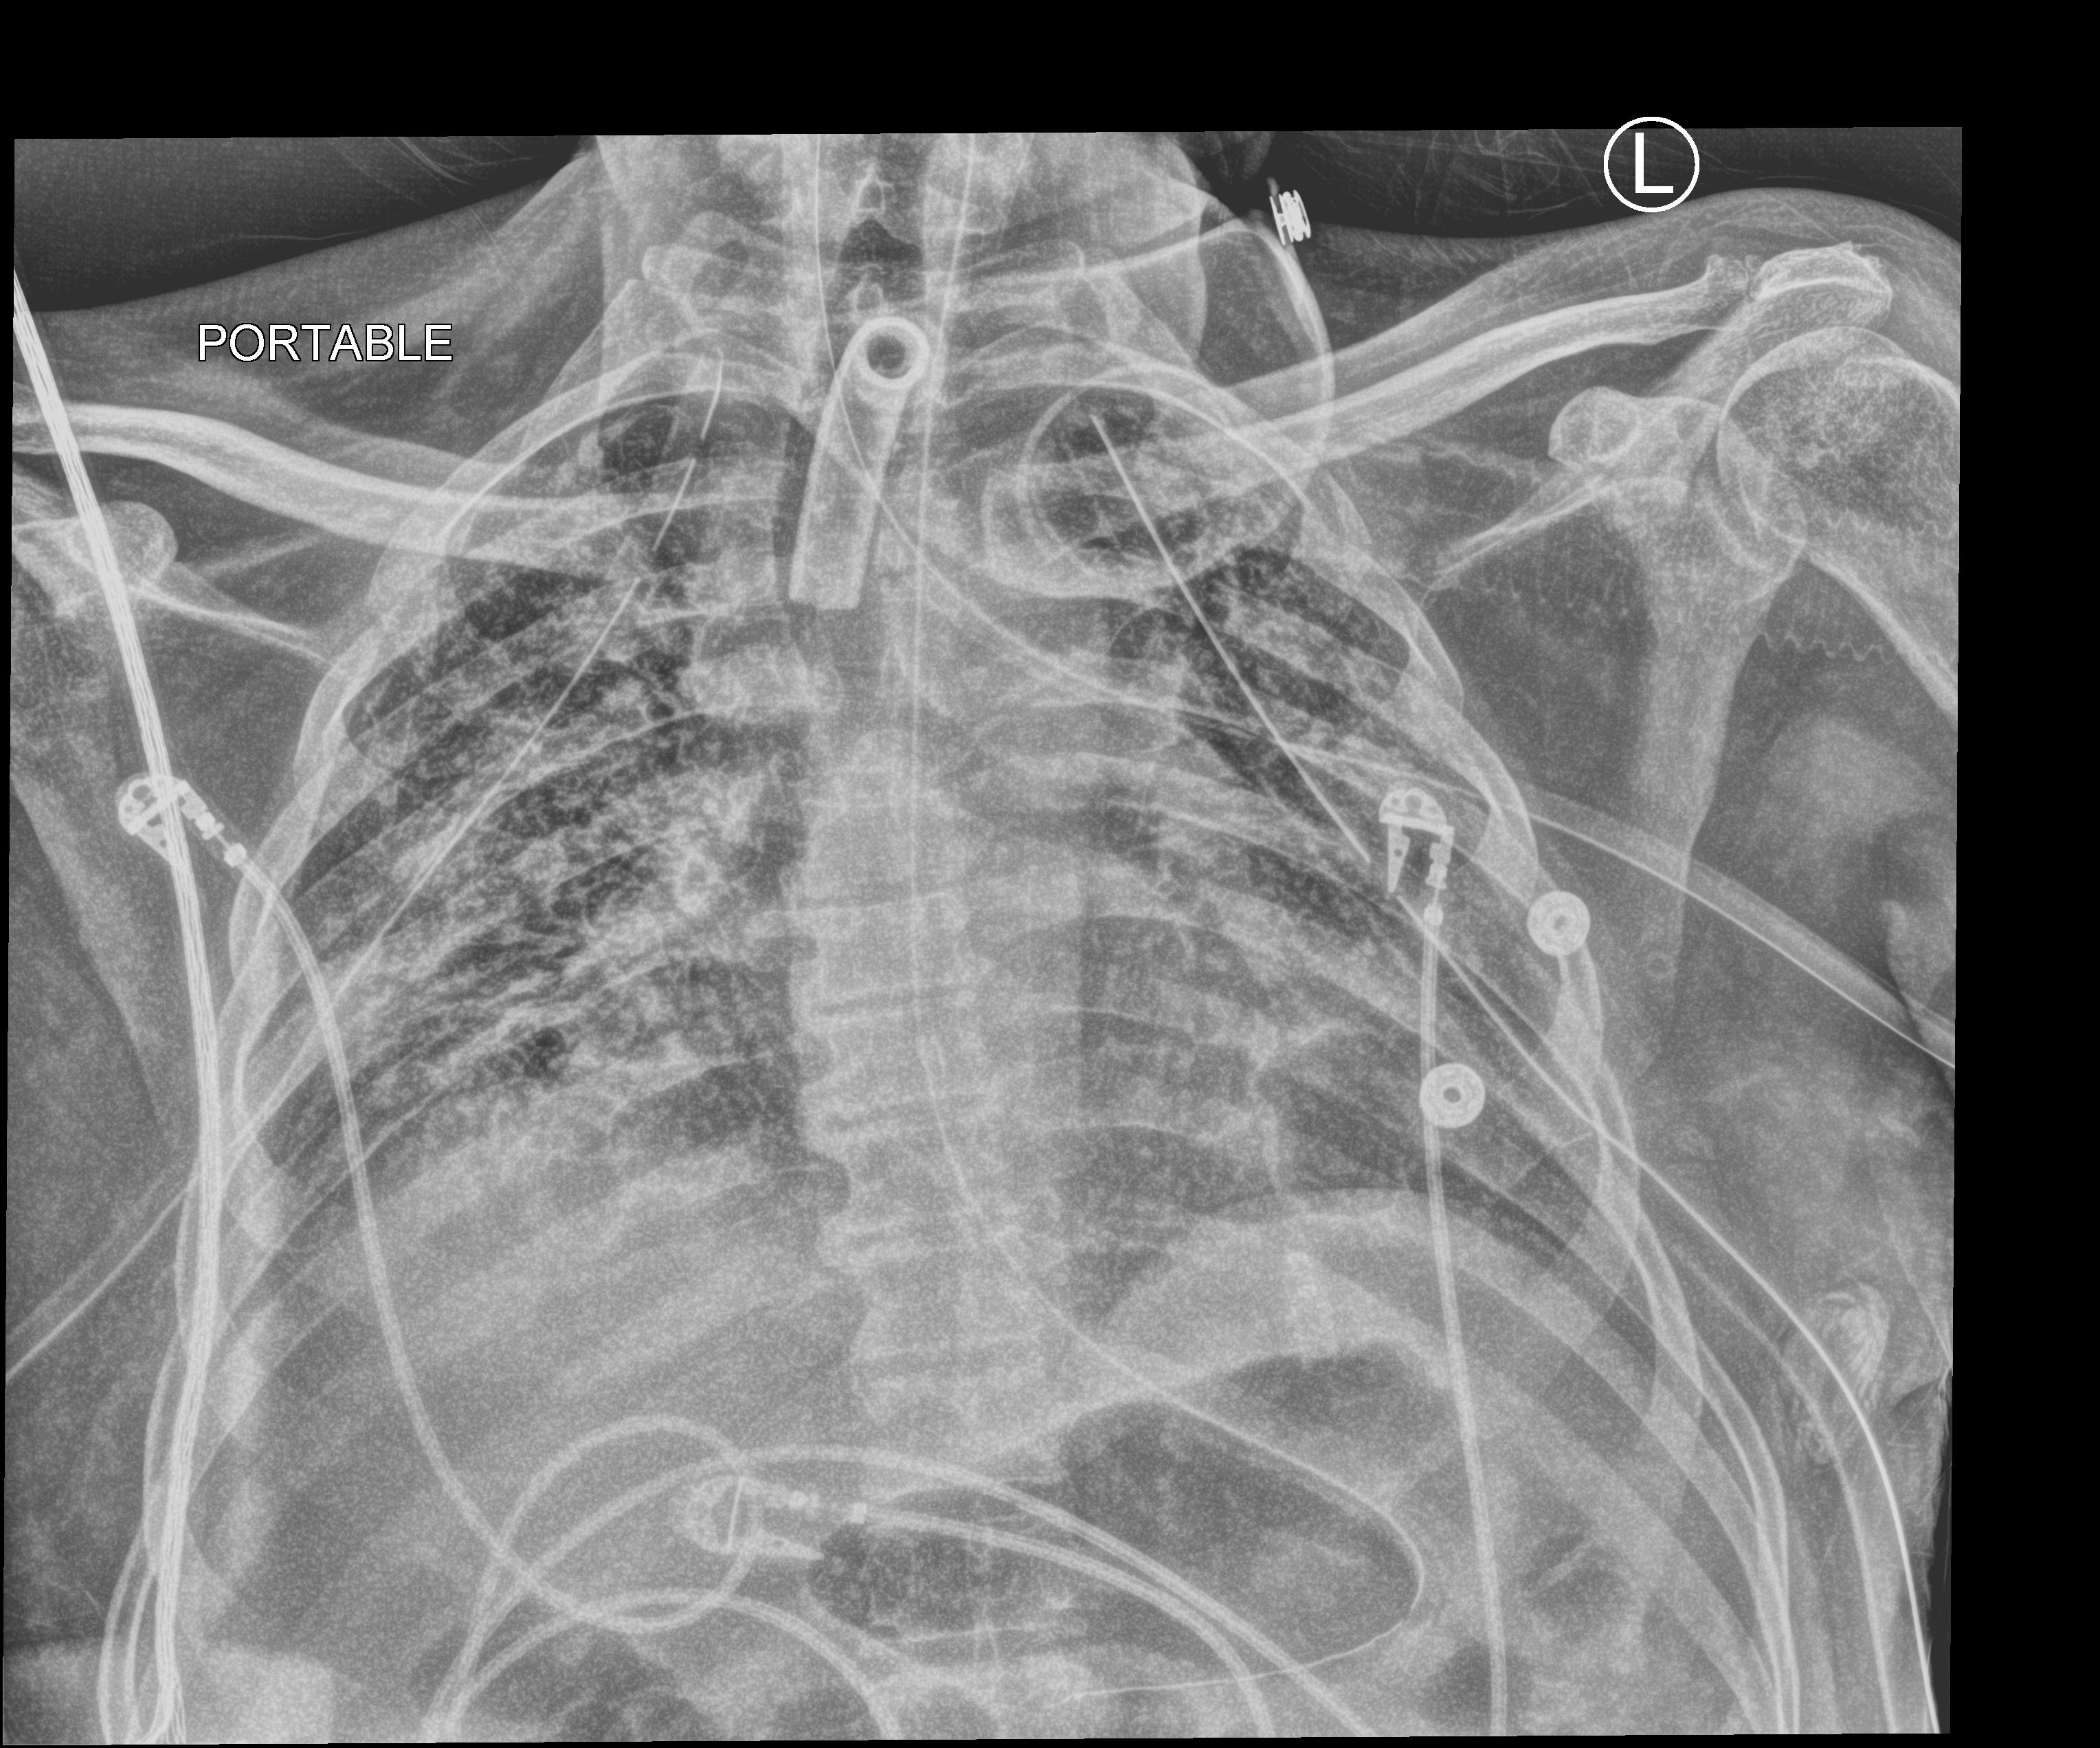
Bedside chest radiograph (computed radiography); anteroposterior (AP) projection. Male patient hospitalised with COVID-19, age 18–59 years.
Admission-level facts for this patient (not findings on this image; timing relative to this image not recorded): smoking status (admission record): never.